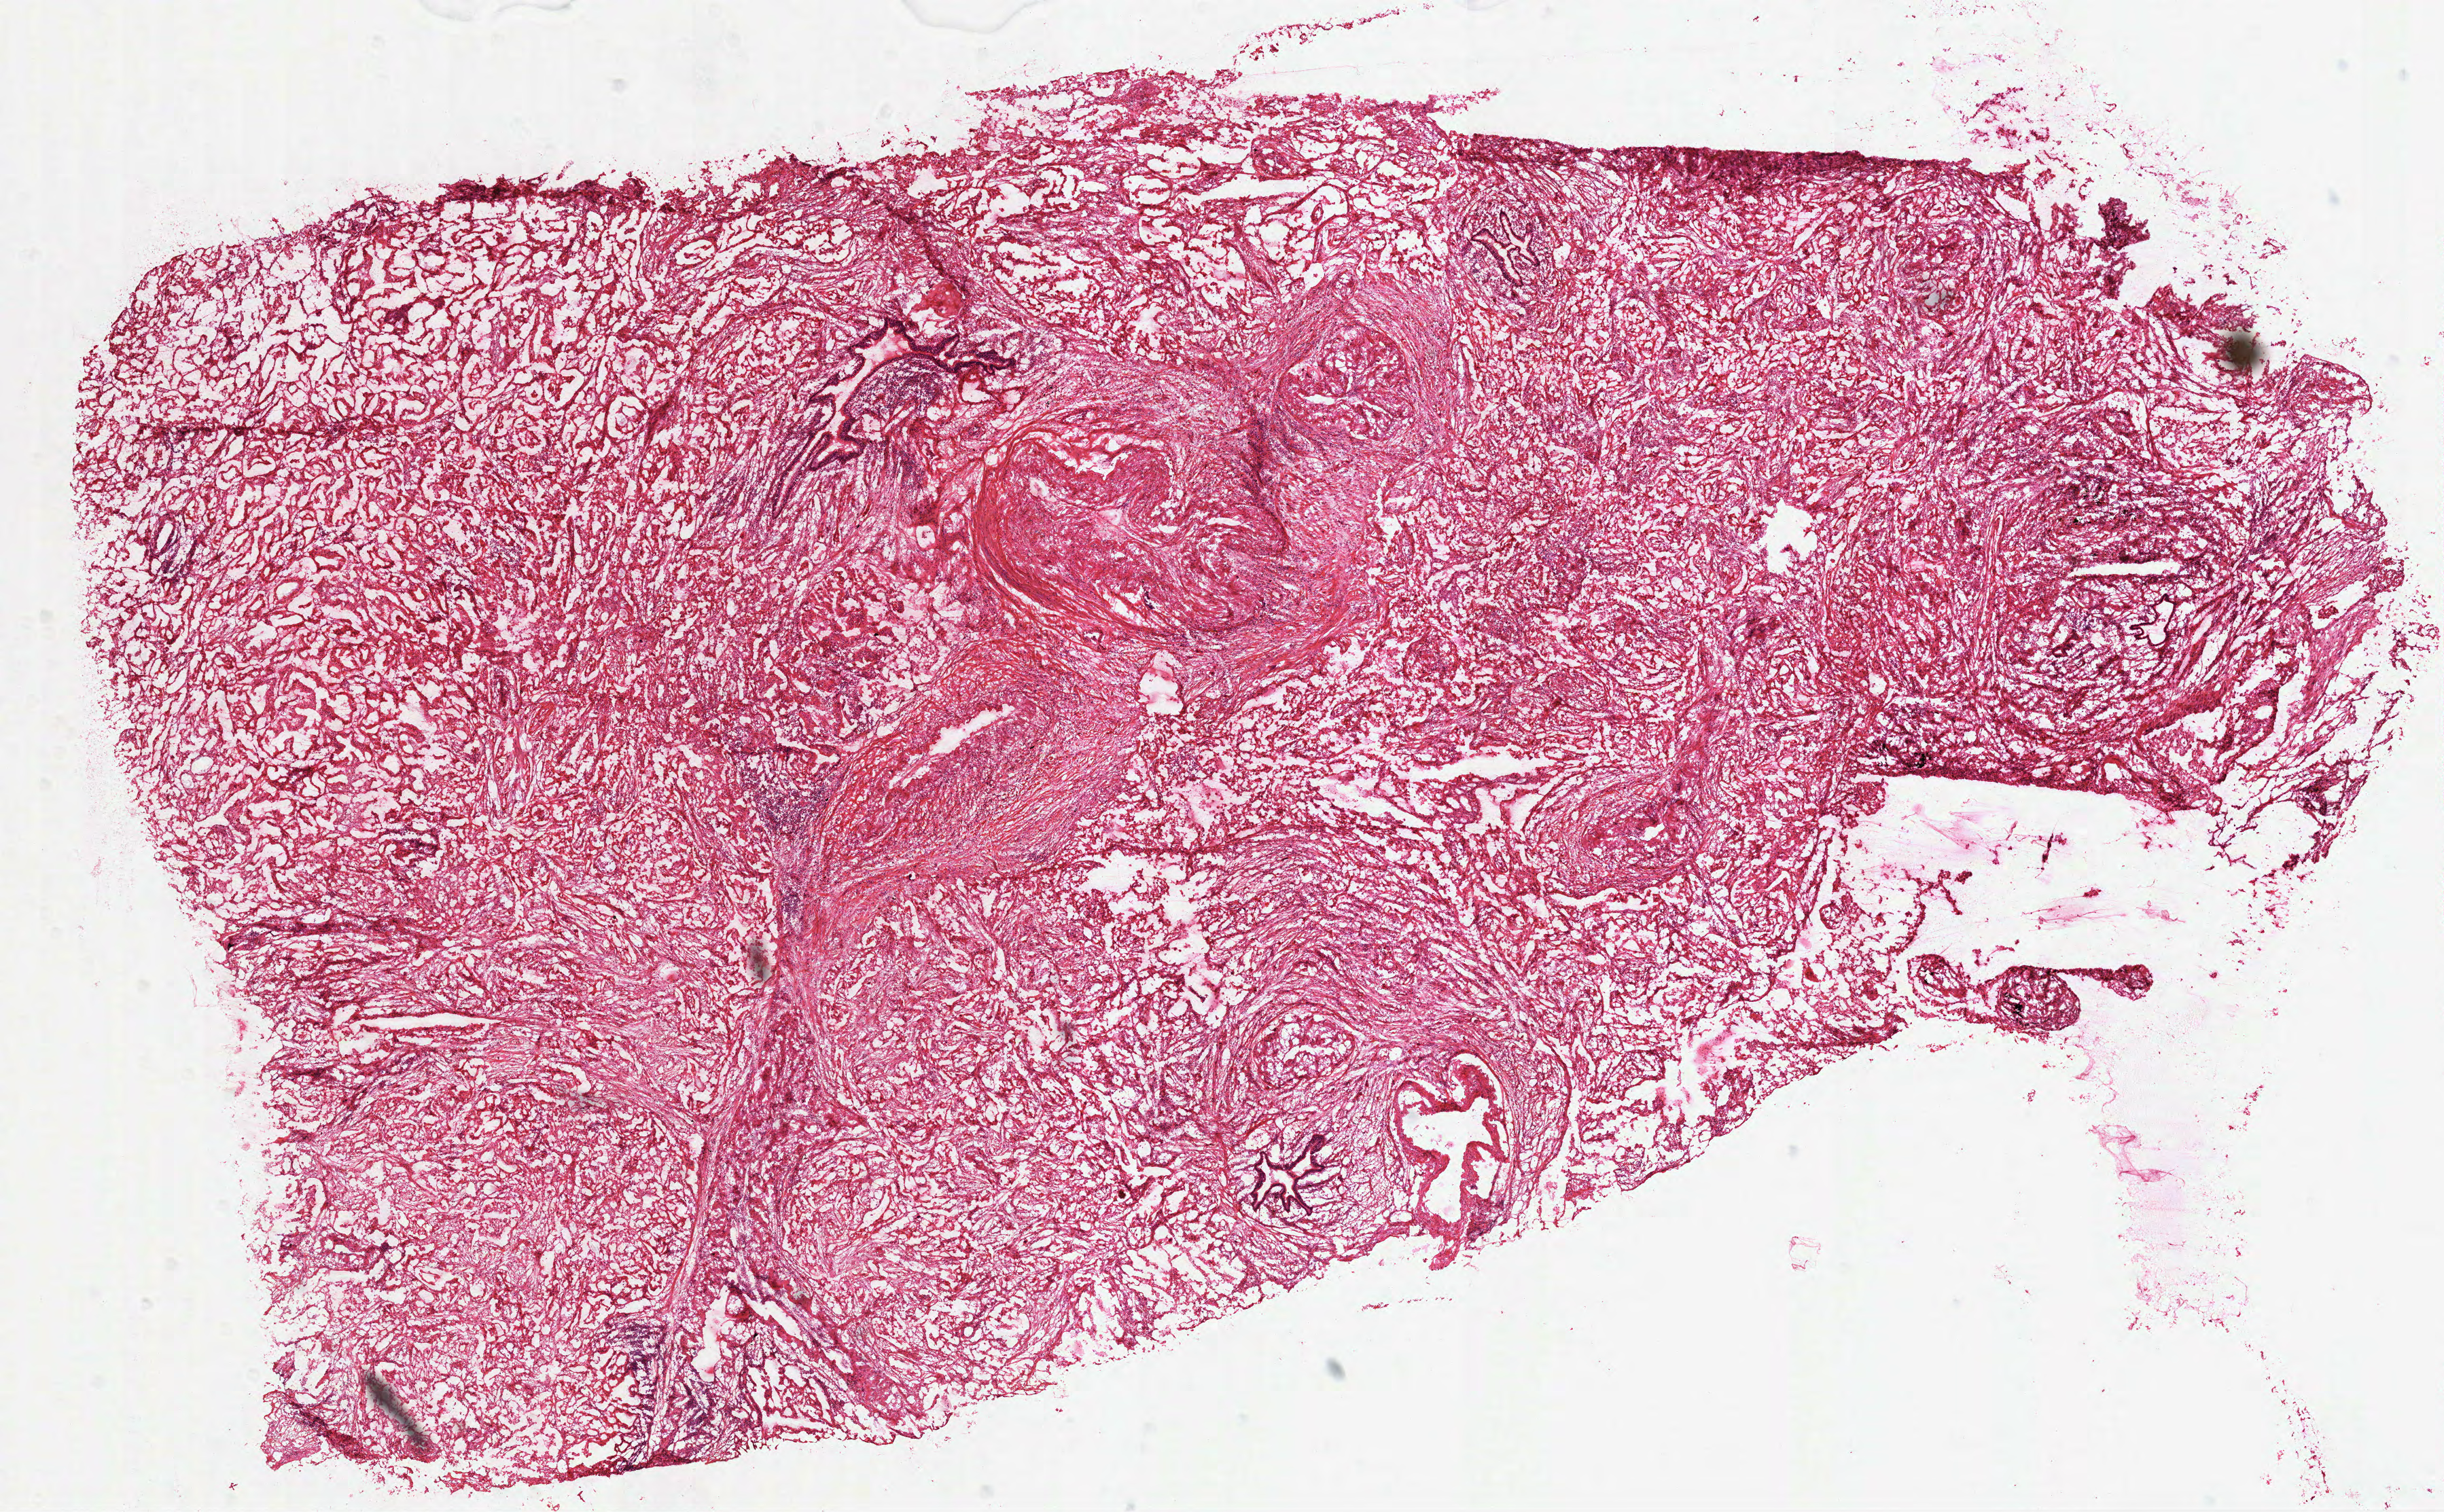
Digitized H&E tissue section (whole slide), a low-resolution overview of the entire scanned area, about 14.5 x 9.0 mm (acquisition: 40x scan), frozen section from the top of the tissue portion, sample: primary tumour, lung. Patient: male, age at initial diagnosis 68 years. Slide review estimates, as recorded: tumour cells 90%, tumour nuclei 70%, normal cells 0%, stromal cells 10%, necrosis 0%. Inflammatory infiltration, as recorded: lymphocyte infiltration 15%.
- histologic diagnosis: Mucinous adenocarcinoma
- AJCC pathologic stage: IIB (7th edition)
- TNM: T3 N0 M0